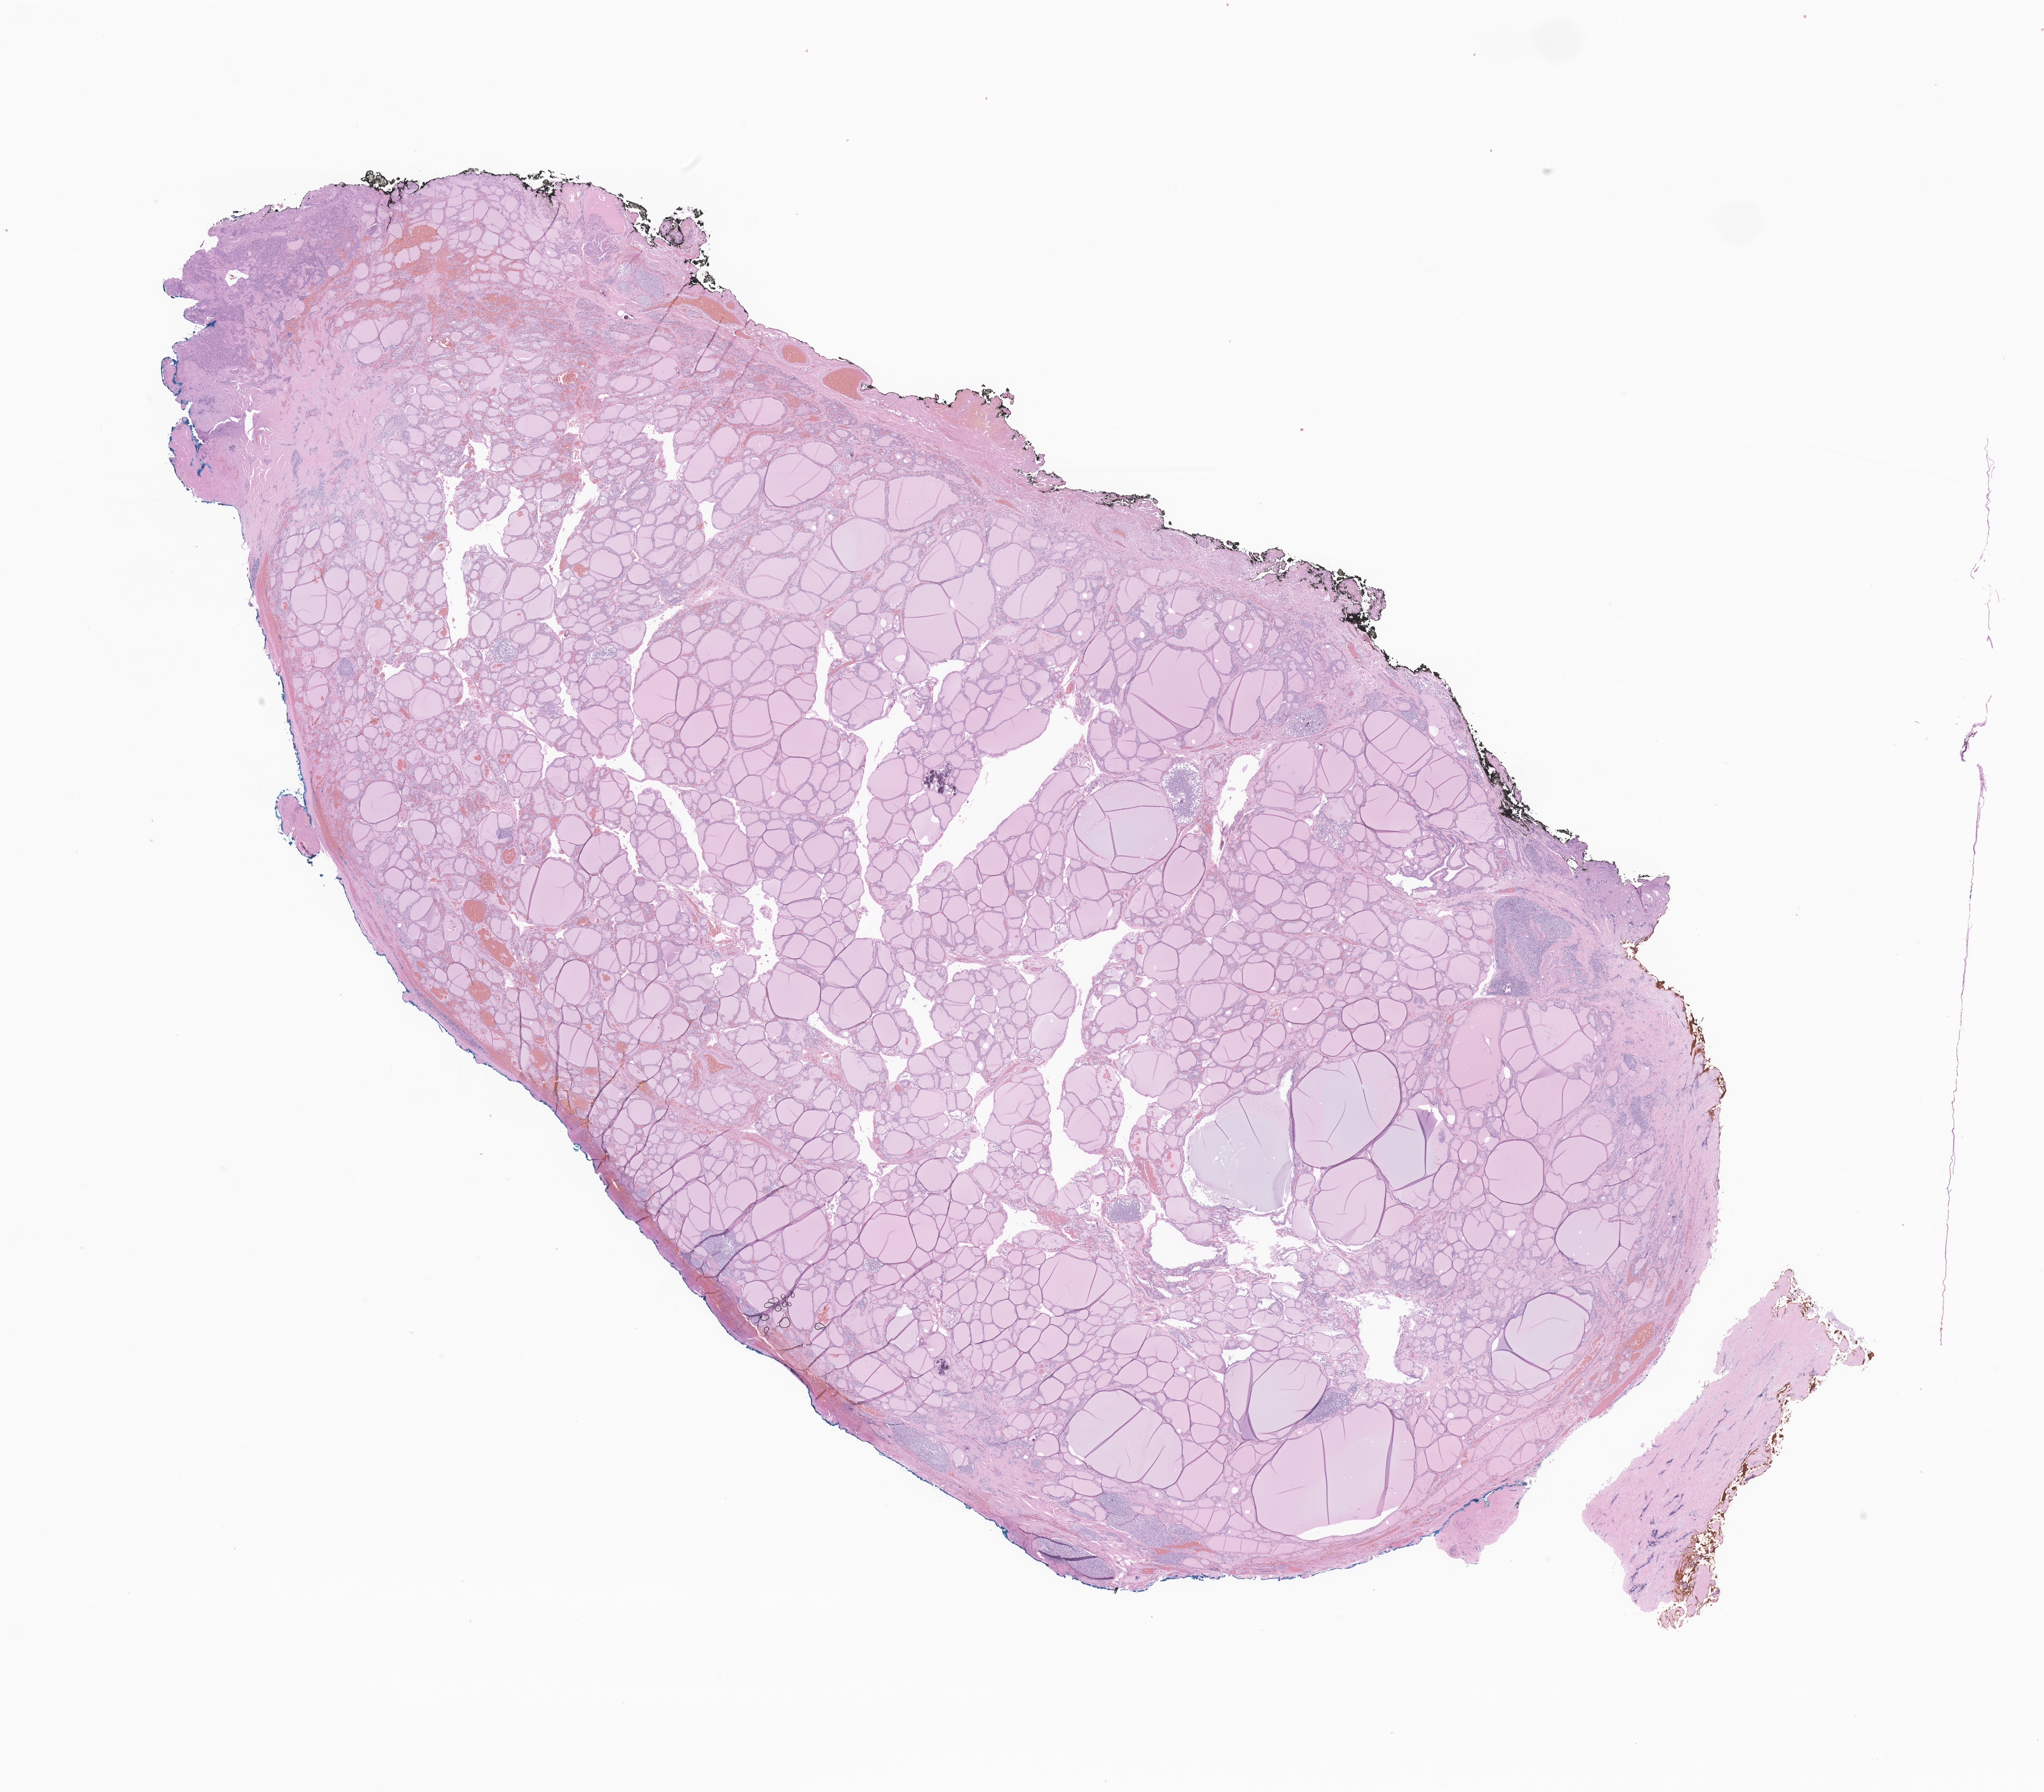
Whole-slide image, haematoxylin and eosin stain of tumor tissue from the thyroid — whole scanned area (about 22.9 x 20.1 mm) shown as a low-resolution overview, formalin-fixed paraffin-embedded section. Patient: female, age 158 months (13 years 2 months).
Diagnosis: Medullary carcinoma, NOS.